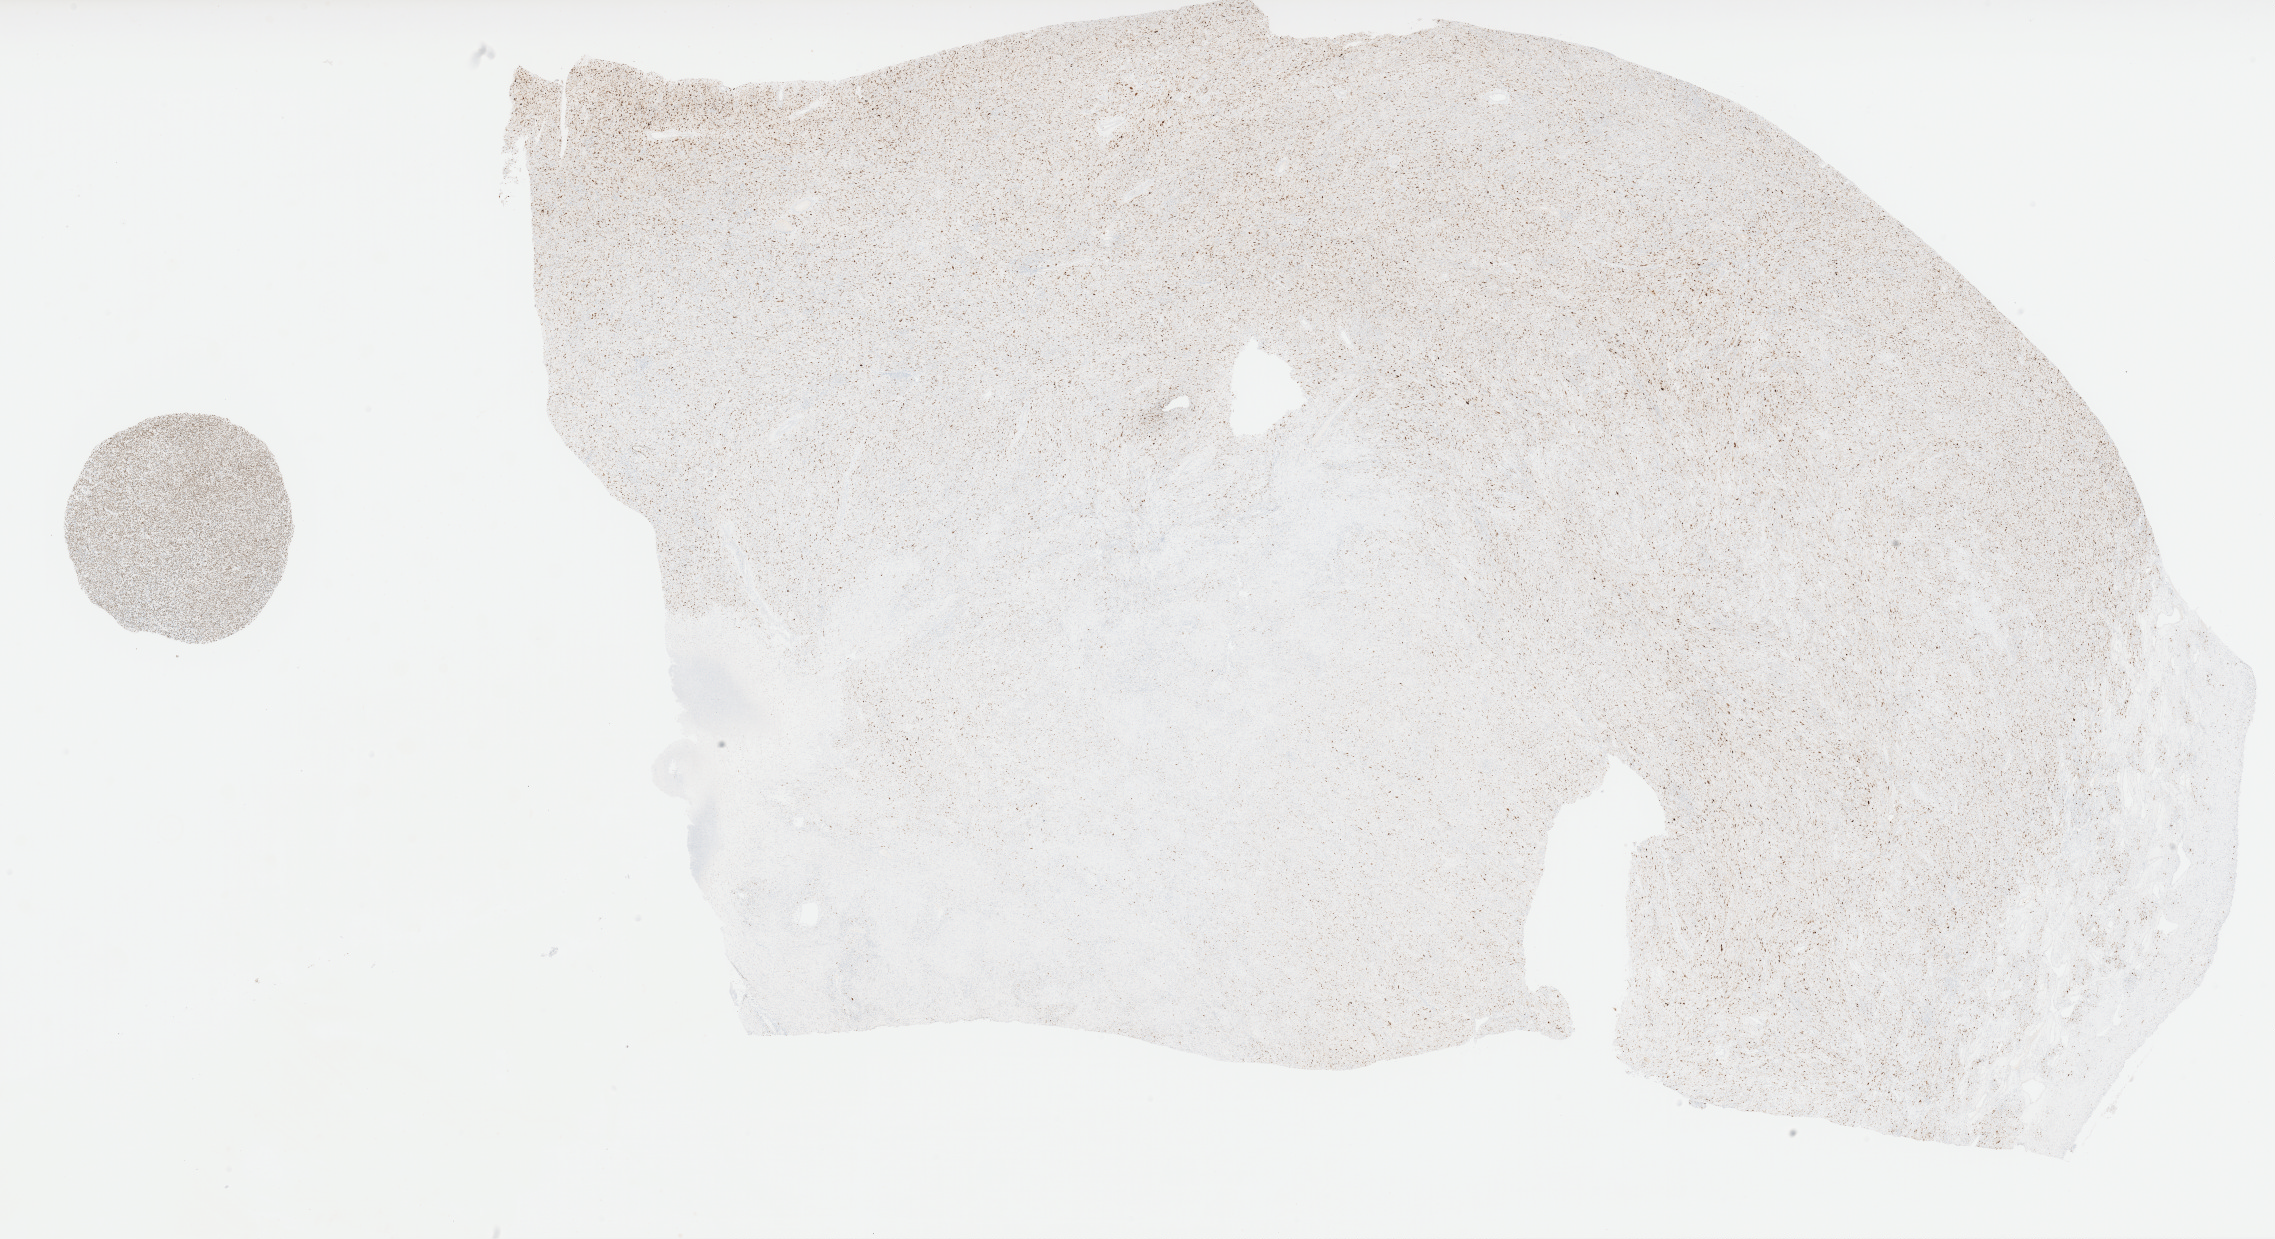
Whole-slide histology image, H&E, low-resolution overview of the scanned area, about 36.4 x 19.8 mm (acquisition: 40x scan); formalin-fixed paraffin-embedded (FFPE) diagnostic section; sample: primary tumour, retroperitoneum and peritoneum. Patient: male, age at initial diagnosis 51 years.
Histologic diagnosis: Dedifferentiated liposarcoma (retroperitoneum).